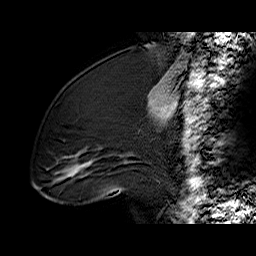
Breast MRI (dynamic contrast-enhanced), one sagittal slice. Slice 25 of 60 in the series (ordered by position). Dynamic contrast-enhanced series, time point 2 of 6 at this slice position (early post-contrast). 1.5 T. TE 6.2 ms, TR 32.4 ms. 4 mm slice thickness. 256 × 256 image matrix. Female patient. From the clinical record (not read from this slice): setting: breast cancer imaged before/during neoadjuvant chemotherapy; receptor status: triple-negative.
Structures marked on this image (semi-automatic segmentation, software-assisted and operator-edited):
- analysis volume of interest (the breast-tissue region the enhancement analysis was run in; not a lesion): bounding box [x1, y1, x2, y2] px = [36, 98, 134, 196]
- tumour enhancement mask (voxels above the 100 % enhancement threshold inside the analysis volume of interest): [73, 162, 127, 175]